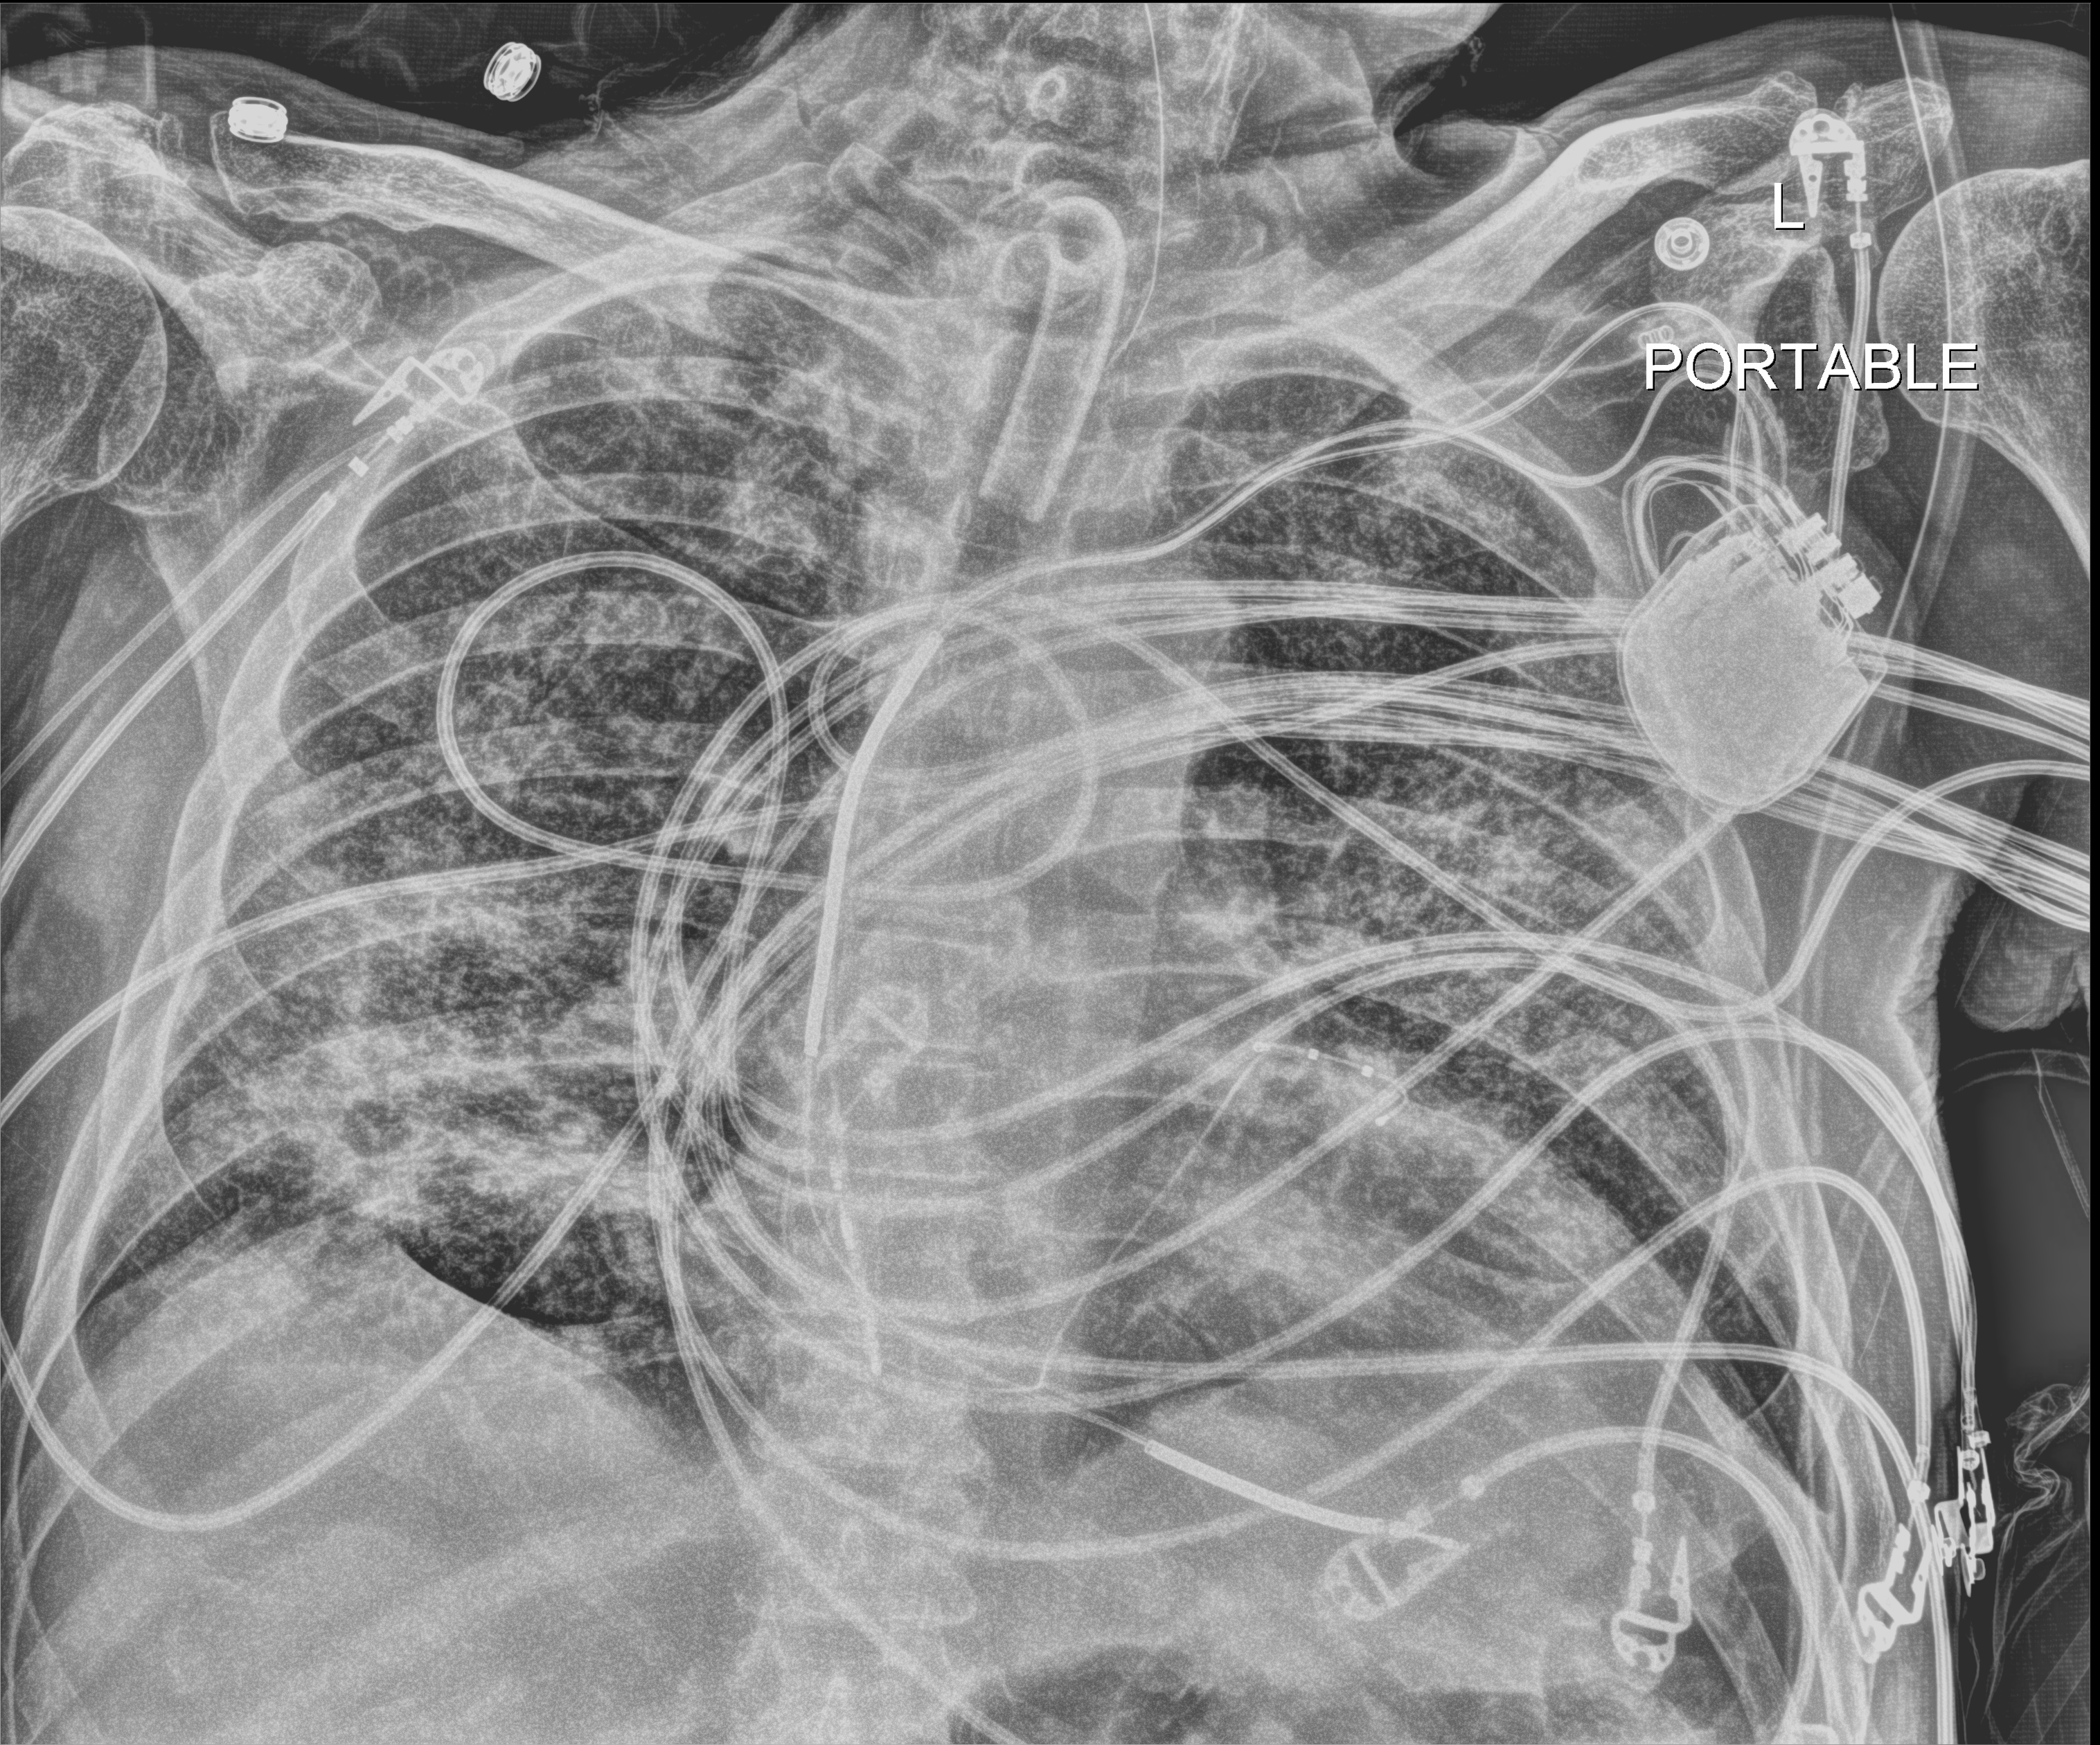
Chest X-ray (portable); anteroposterior (AP) projection. Male patient hospitalised with COVID-19, age 60–74 years.
From the hospital-stay record, not from the radiograph (when in the stay this image was taken is not recorded):
- admitted to intensive care during this hospital stay: yes
- mechanically ventilated during this hospital stay: yes